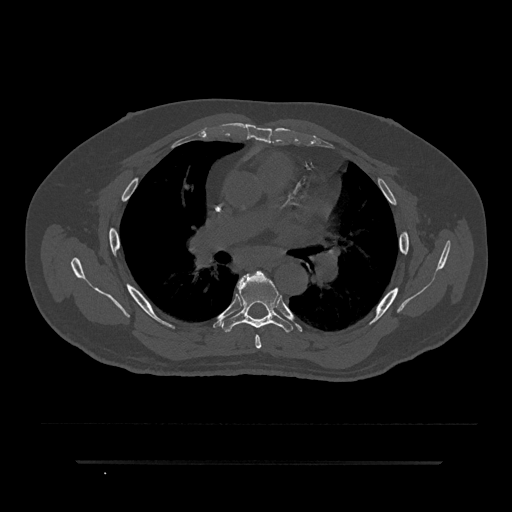
CT including the spine, one axial slice. Position 538 of 797 along the scan axis. Bone window (W 1800 / L 400 HU). 0.5 mm slice thickness. 512 × 512 image matrix. Male patient, age 59 years. Case-level facts recorded for this patient, not image findings: primary cancer: bile ducts.
Annotated regions visible in this slice (semi-automatically segmented with operator editing):
- T5 vertebra: bounding box [x1, y1, x2, y2] px = [254, 272, 264, 349]
- T6 vertebra: [220, 271, 293, 333]